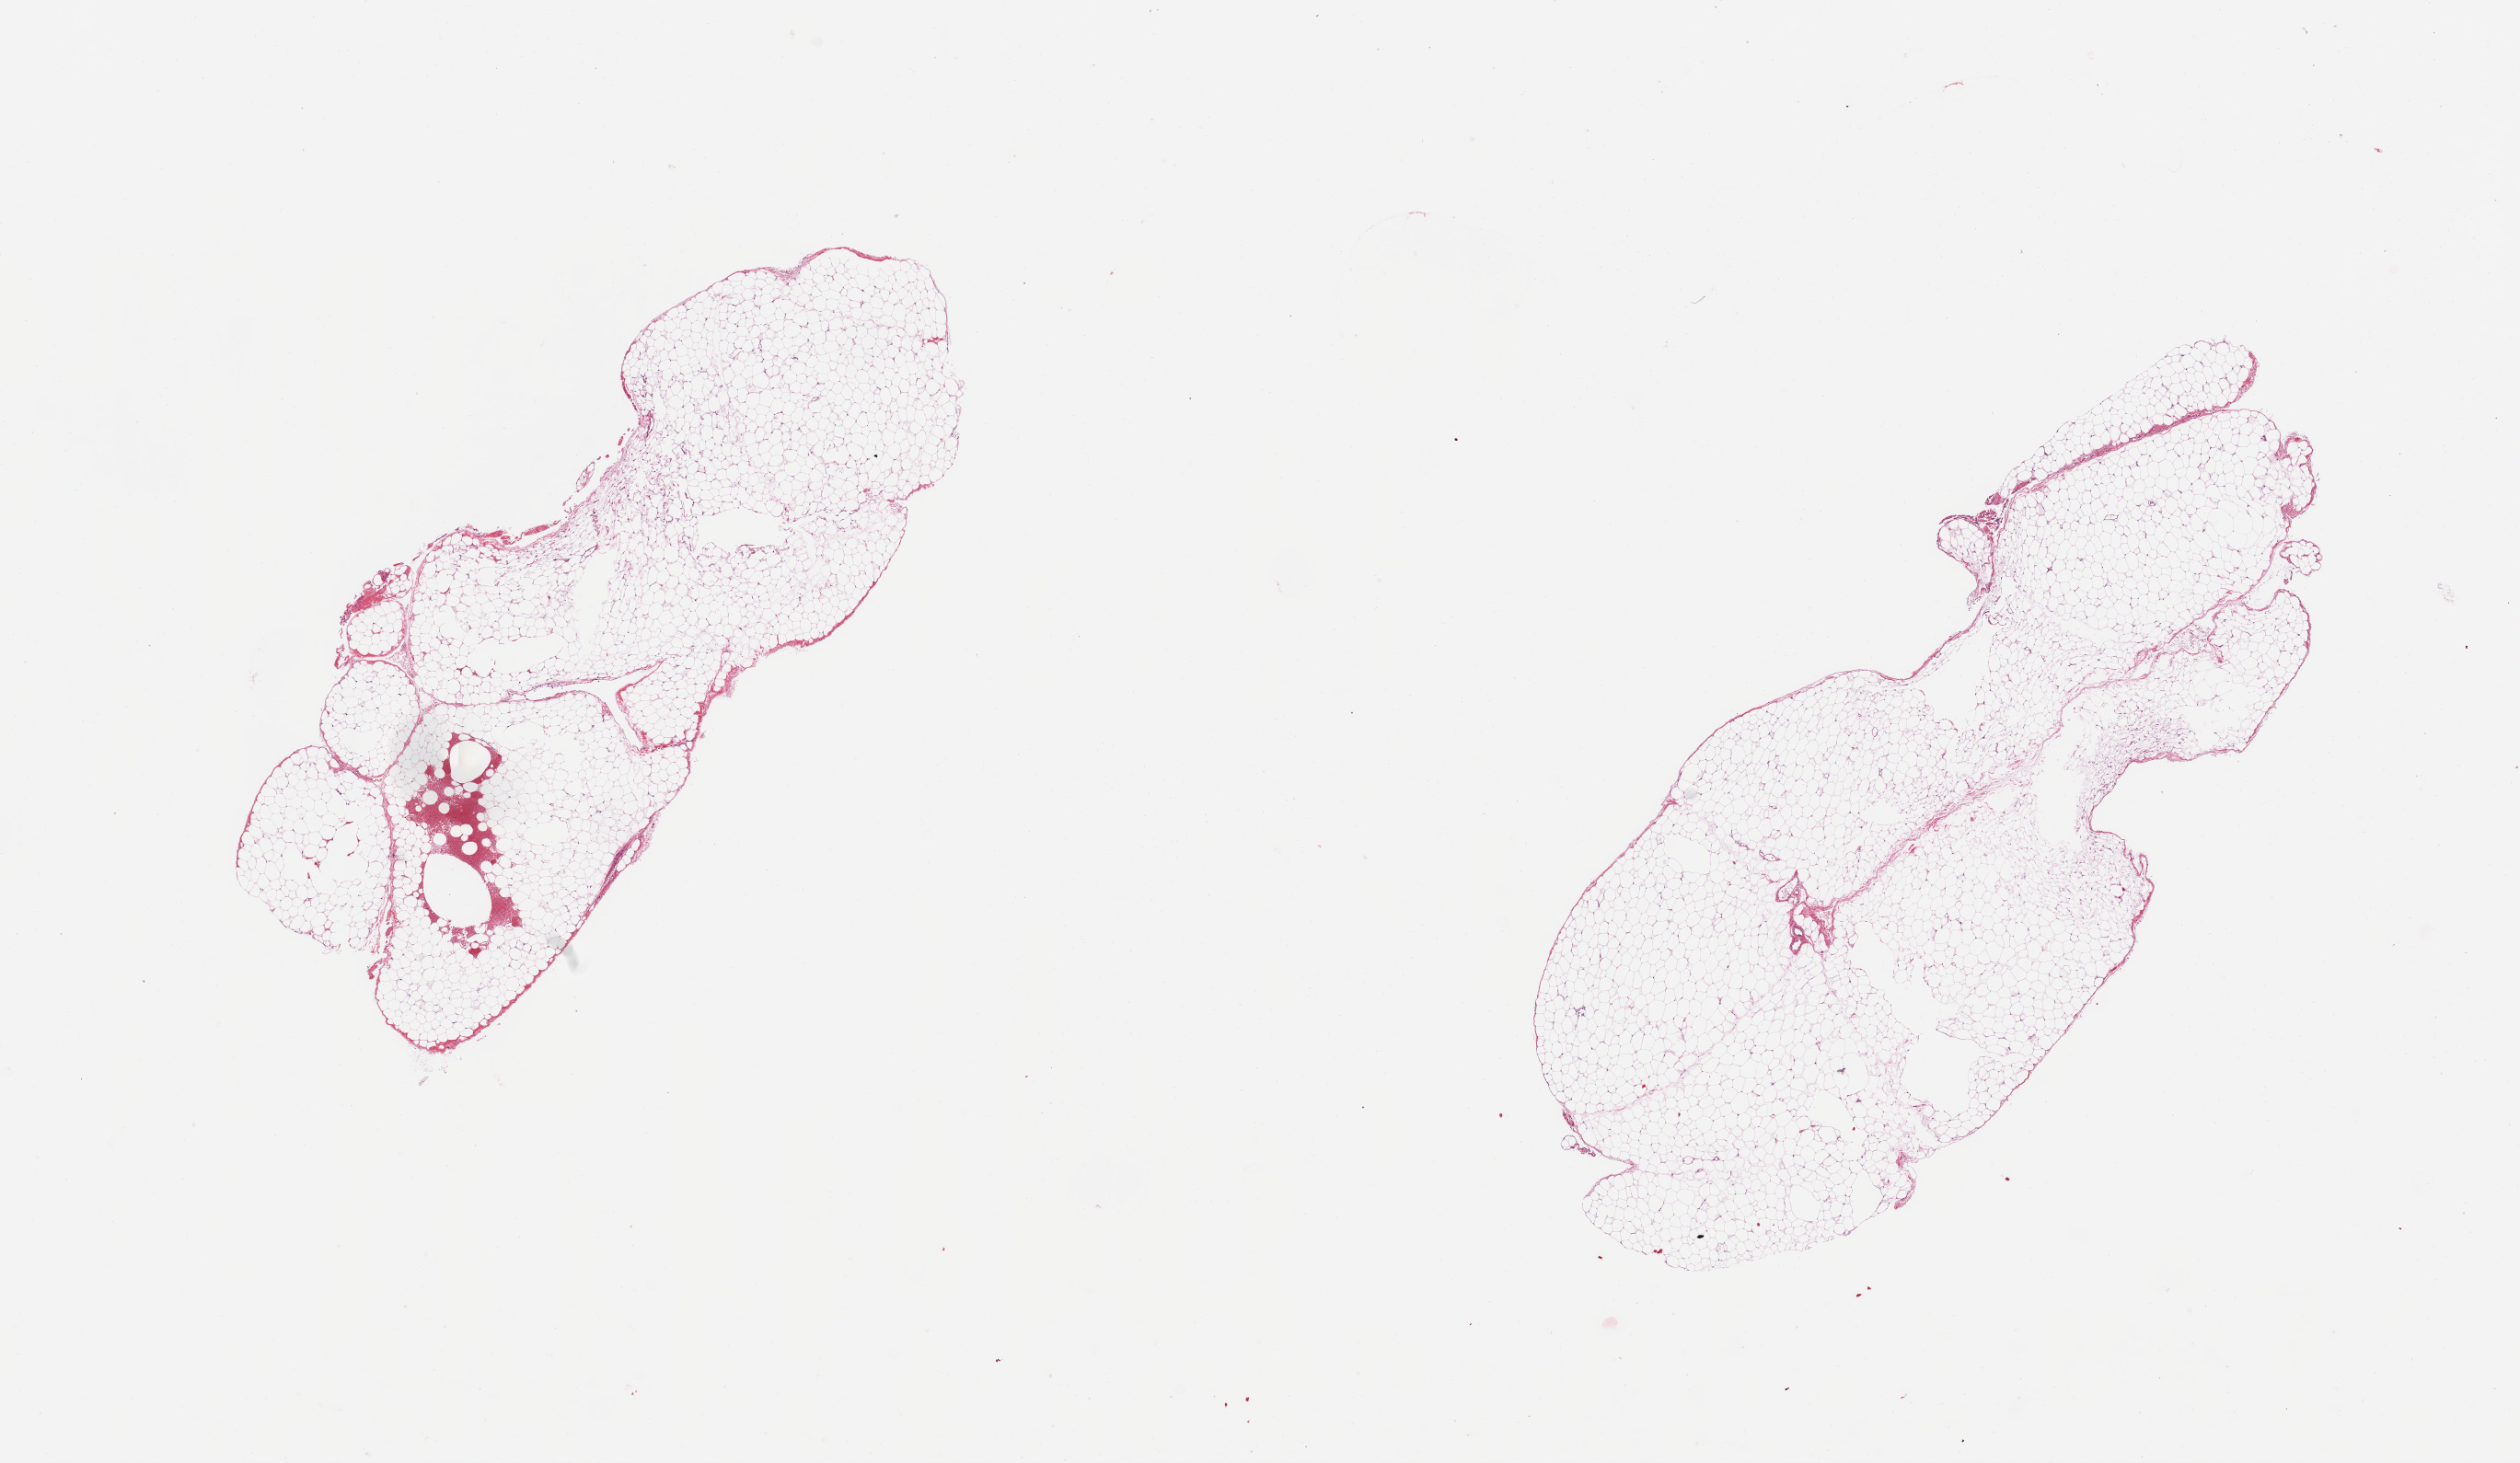
Digitized haematoxylin and eosin-stained section — low-resolution overview of the scanned area, about 21.7 x 12.6 mm. PAXgene-fixed, paraffin-embedded tissue. Sampled site (target tissue): omentum. Tissue donor sample. Male donor.
- pathologist's review note for this sample: 2 pieces; mature fat